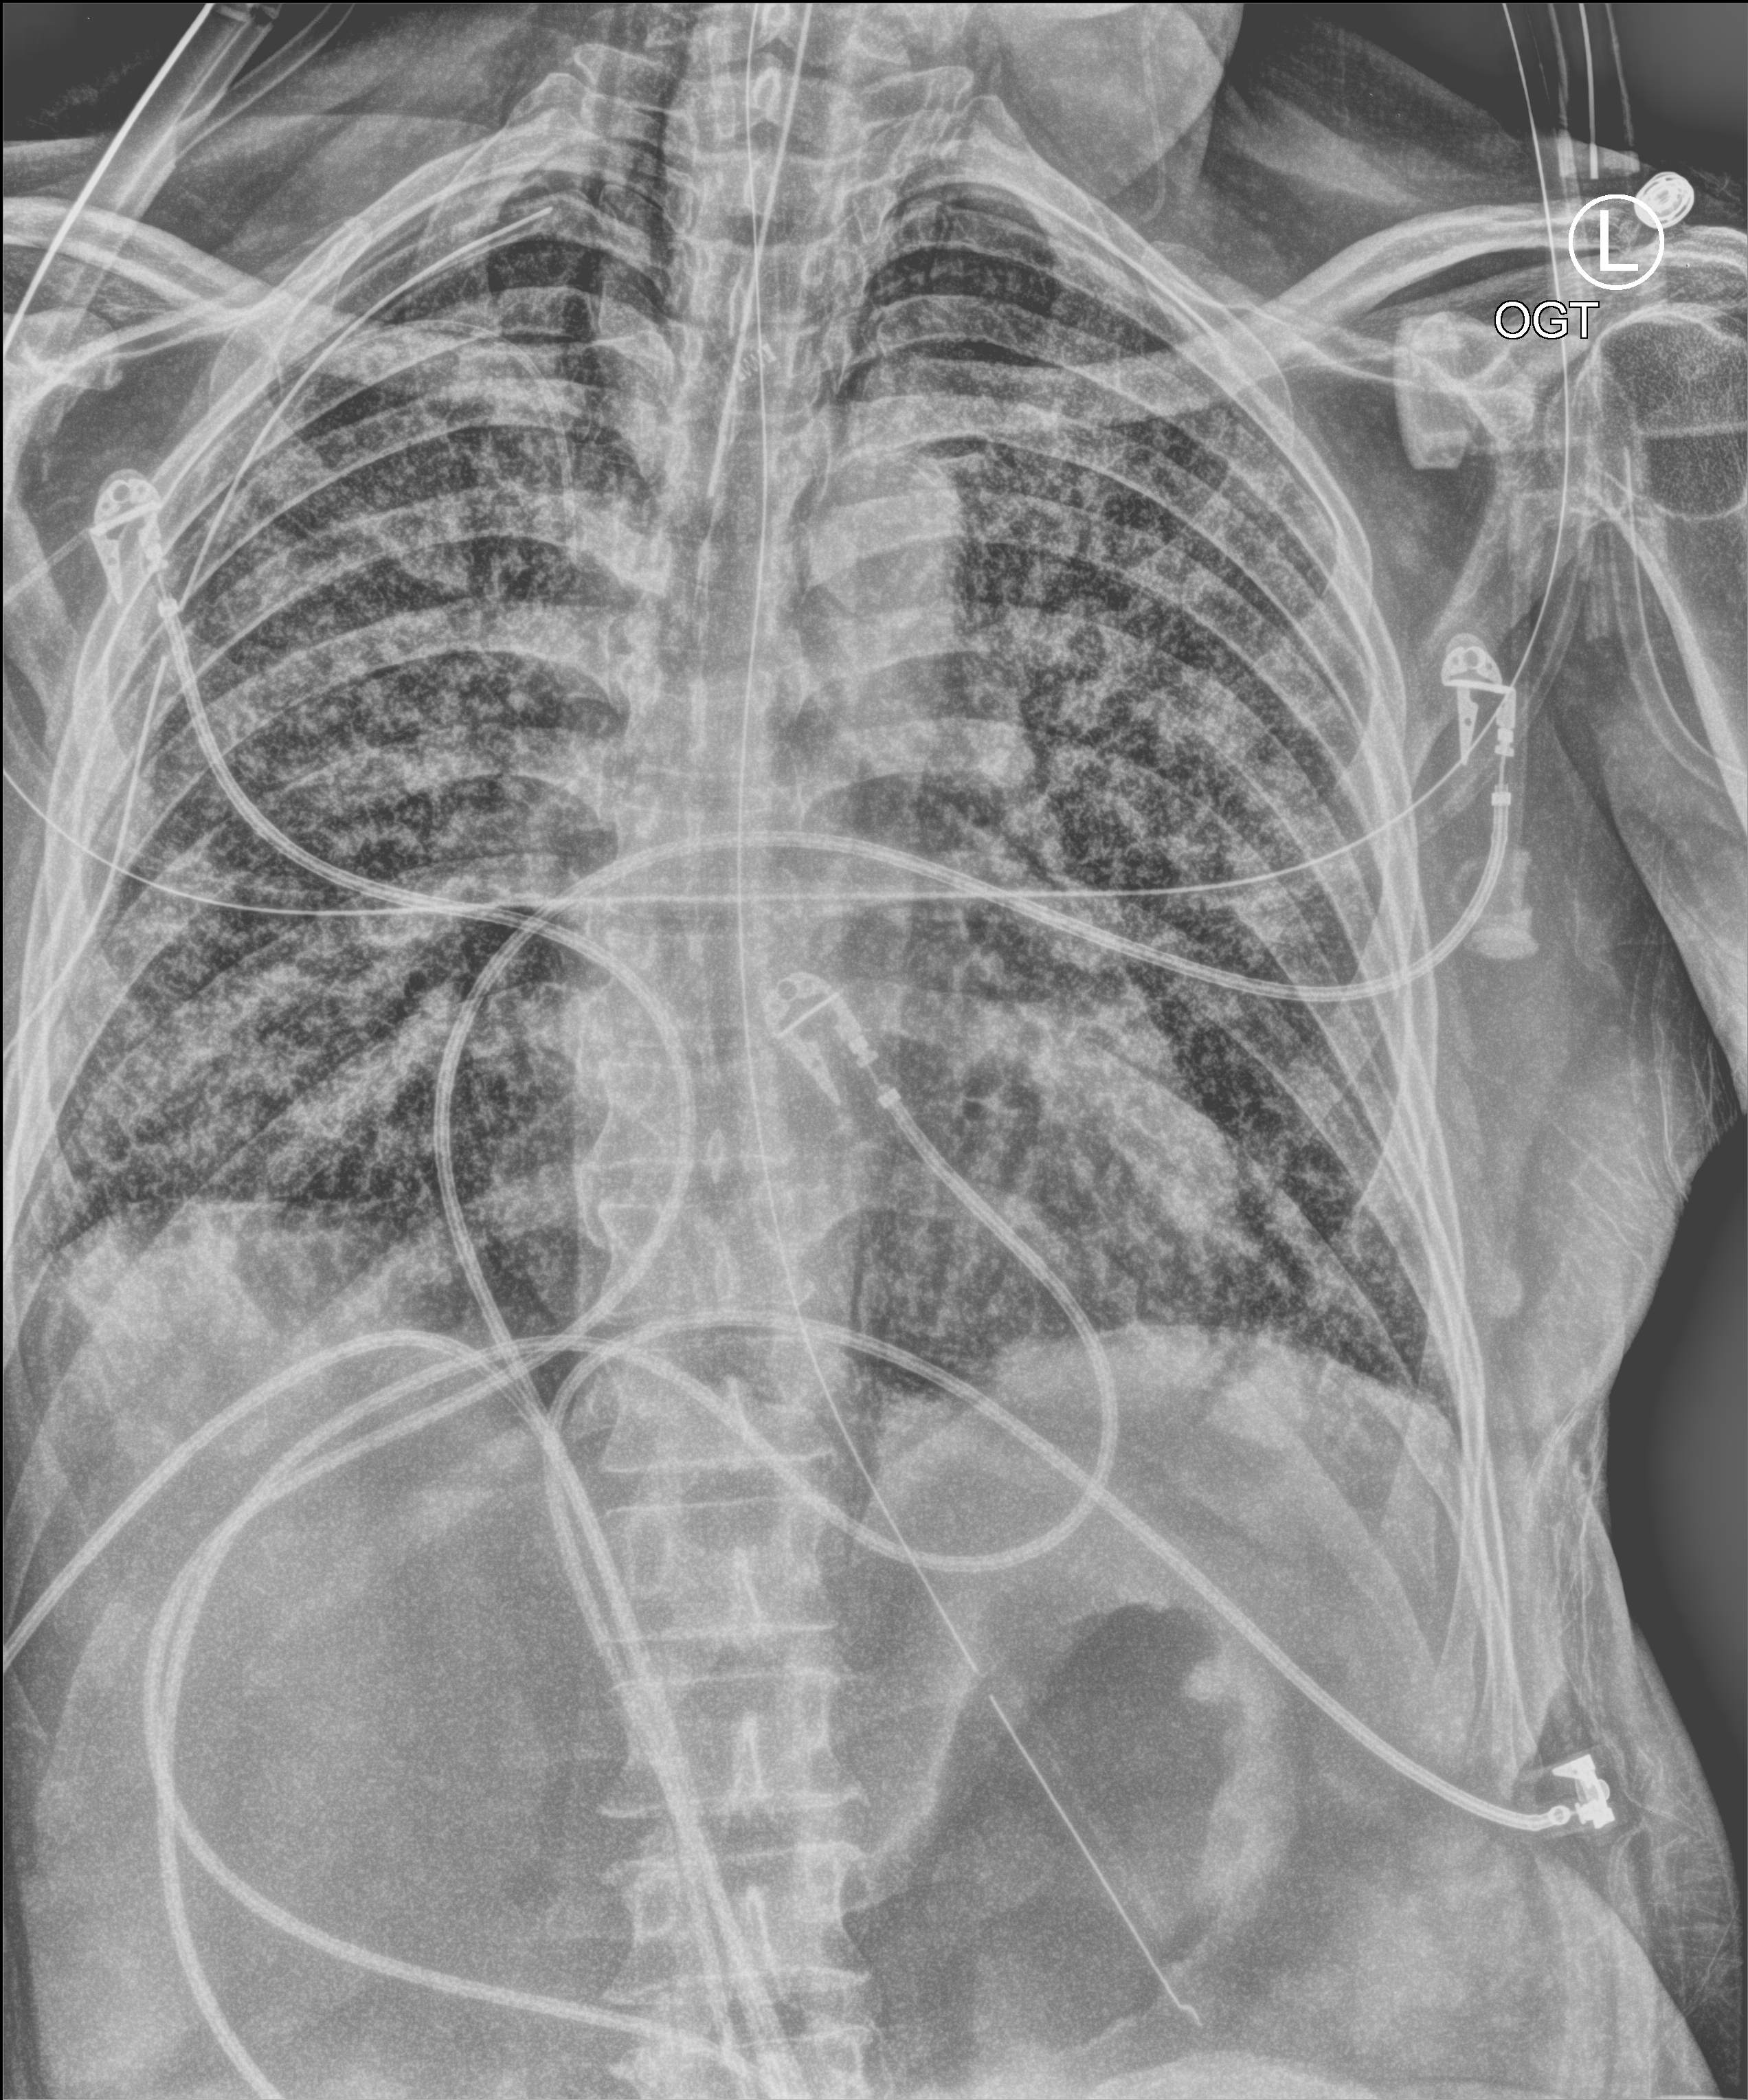
Chest X-ray (portable); anteroposterior (AP) projection. Patient hospitalised with COVID-19; male, aged 60–74 years.
Admission-level facts for this patient (not findings on this image; timing relative to this image not recorded): mechanically ventilated during this hospital stay: yes; admitted to intensive care during this hospital stay: yes; length of hospital stay: 65 days.